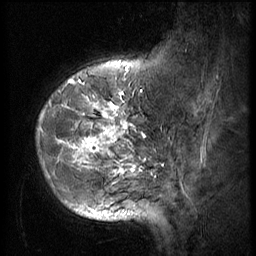
Breast MRI (dynamic contrast-enhanced), one sagittal slice. Slice 14 of 56 in the series (ordered by position). 3 images stored at this slice position (order not interpretable as contrast timing). 1.5 T. TE 4.2 ms, TR 9 ms. 2.5 mm slice thickness. 256 × 256 image matrix, field of view 180 × 180 mm. Patient: female, 49 years. Case-level facts recorded for this patient, not image findings: setting: breast cancer imaged before/during neoadjuvant chemotherapy; receptor status: HER2-positive.
Outlined on this slice (semi-automatically segmented with operator editing):
- analysis volume of interest (the breast-tissue region the enhancement analysis was run in; not a lesion): bounding box (x1, y1, x2, y2) in pixels: (31, 79, 150, 203)
- tumour enhancement mask (voxels above the 140 % enhancement threshold inside the analysis volume of interest): (40, 79, 143, 174)